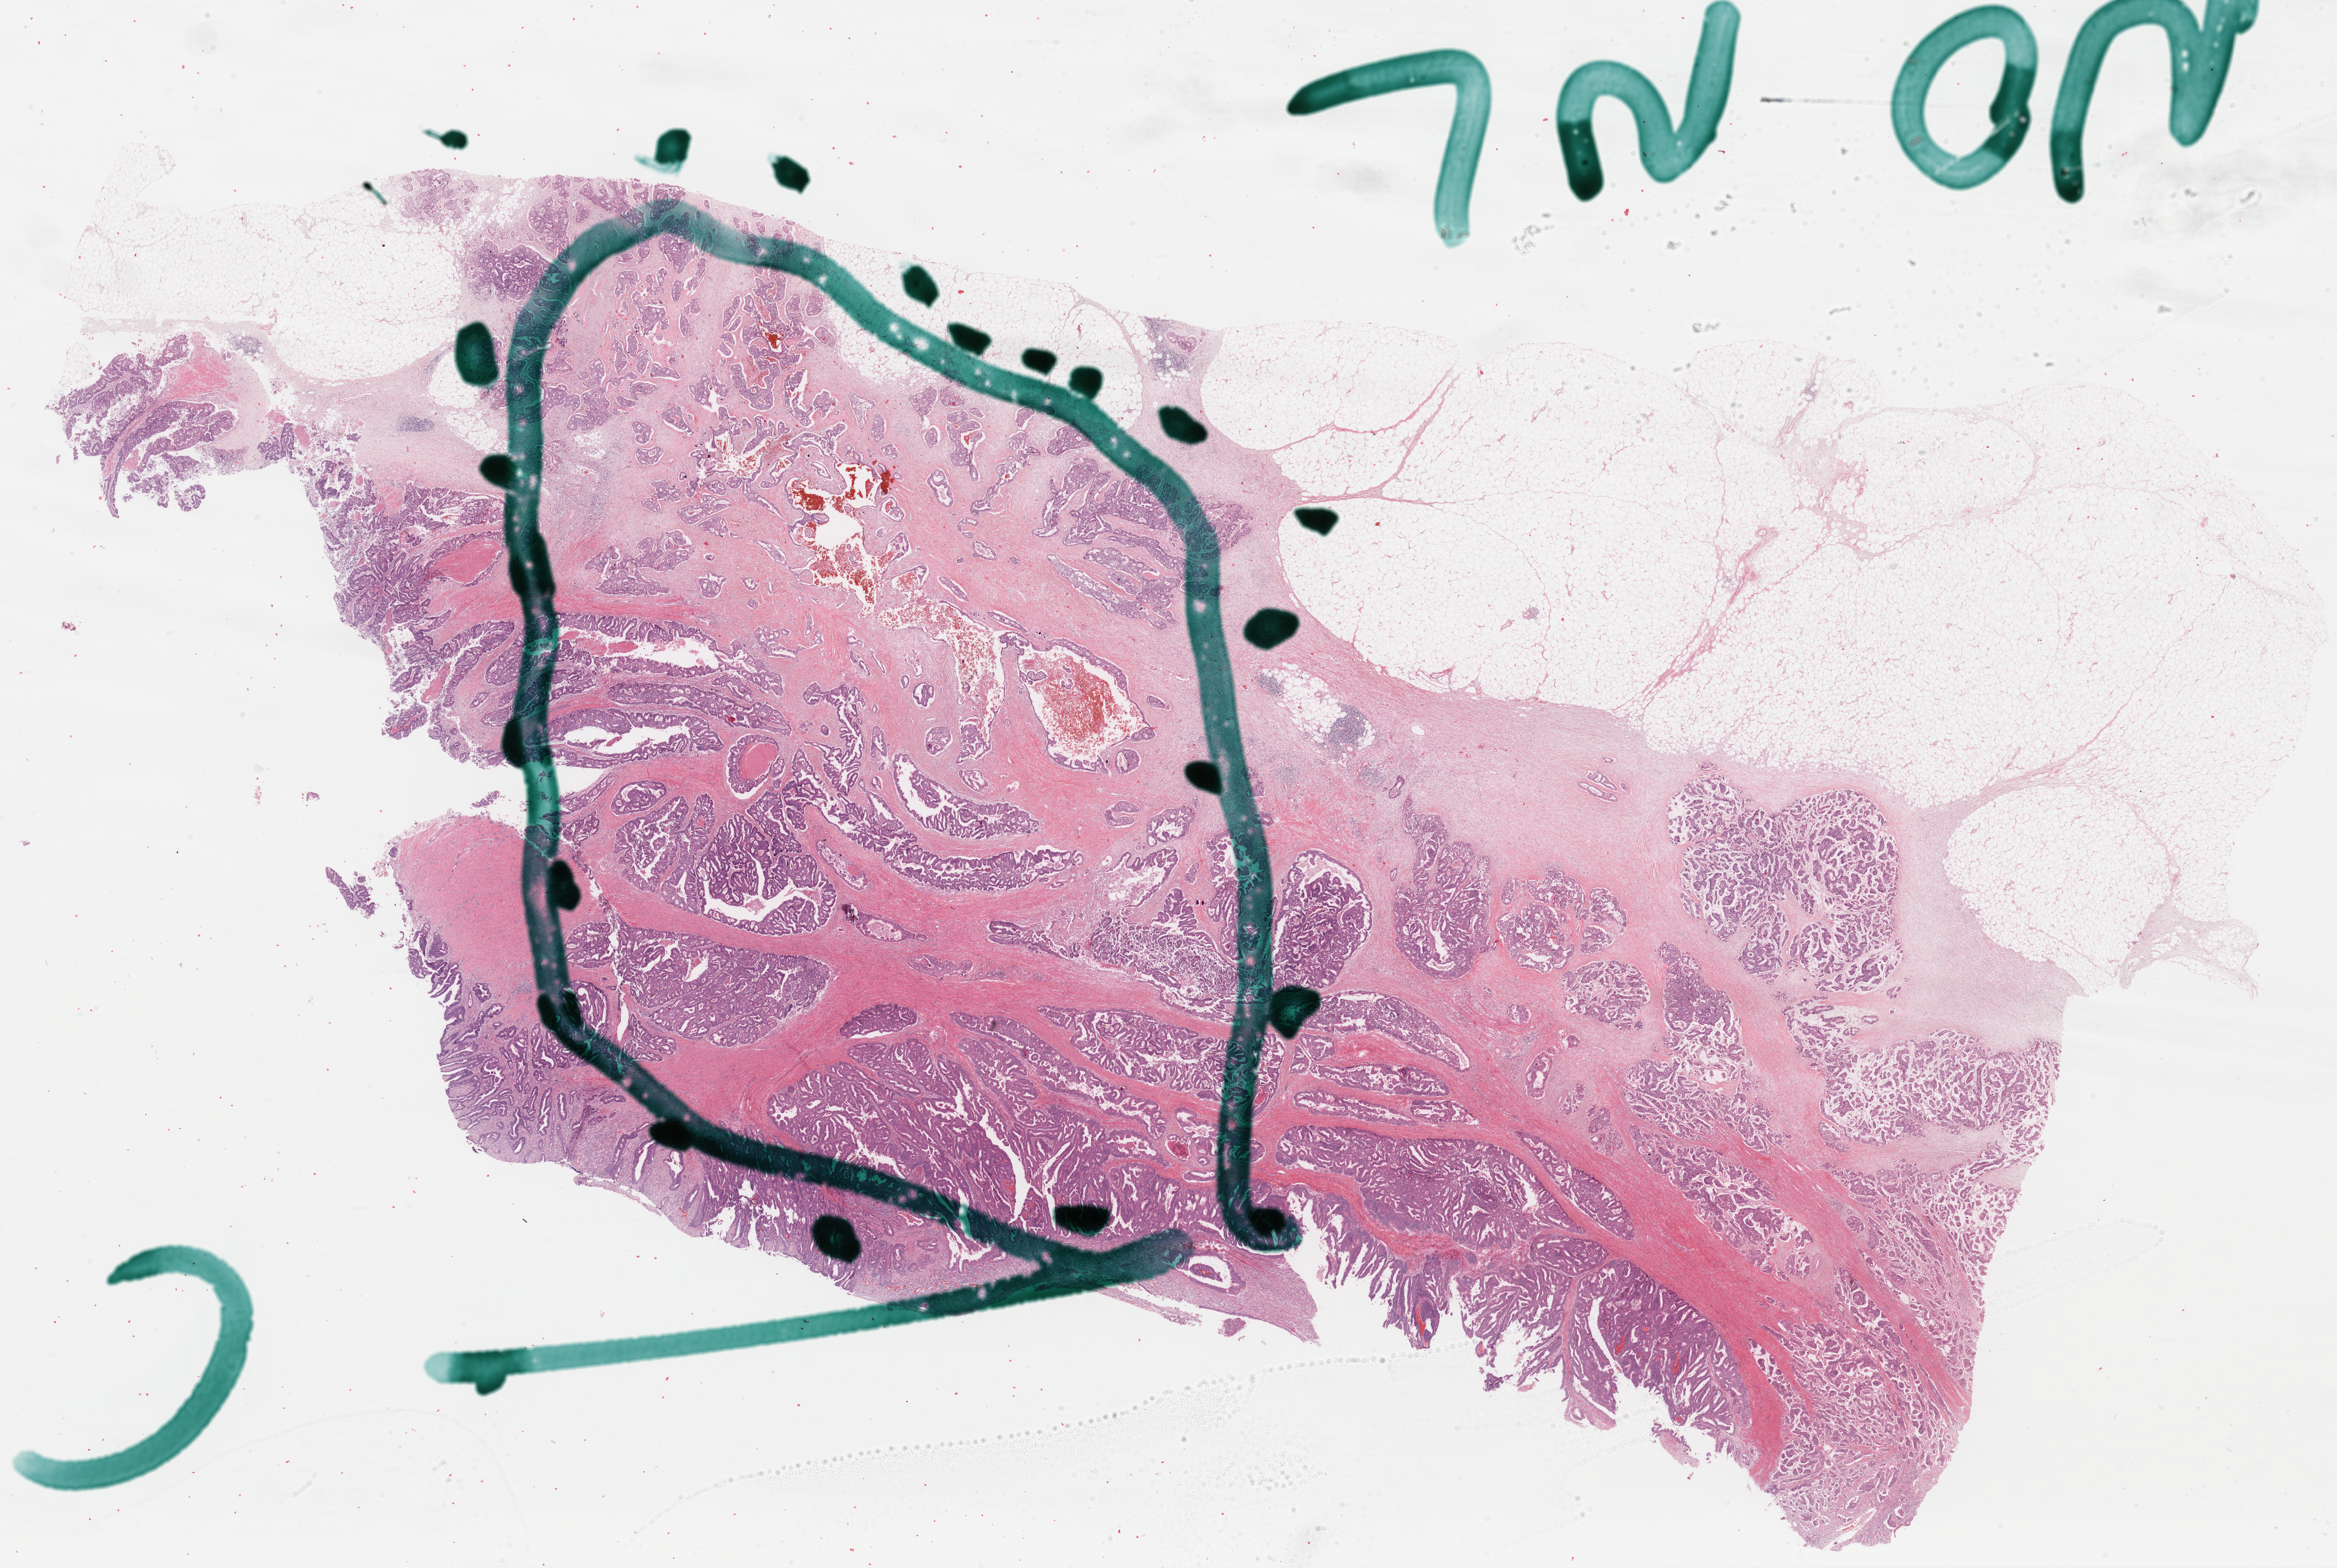
H&E-stained whole-slide image, shown as a low-resolution overview of the whole scanned area (about 31.5 x 21.1 mm). FFPE section. Primary tumour sample from the rectum. Male, age 75 years at initial diagnosis.
Histologic diagnosis: Adenocarcinoma, NOS.